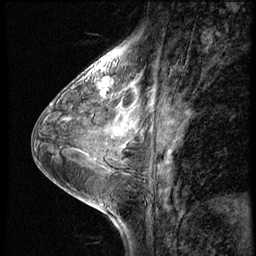
Breast MRI (dynamic contrast-enhanced), one sagittal slice. Position 22 of 56 along the scan axis. 4 images stored at this slice position (order not interpretable as contrast timing). 1.5 T. TE 4.2 ms, TR 8.9 ms. 2.5 mm slice thickness. 256 × 256 image matrix, field of view 200 × 200 mm. Patient: female, 38 years. Case-level facts recorded for this patient, not image findings: setting: breast cancer imaged before/during neoadjuvant chemotherapy; receptor status: triple-negative.
Outlined on this slice (semi-automatic segmentation, software-assisted and operator-edited):
- analysis volume of interest (the breast-tissue region the enhancement analysis was run in; not a lesion): bounding box (x1, y1, x2, y2) in pixels: (88, 73, 115, 102)
- tumour enhancement mask (voxels above the 140 % enhancement threshold inside the analysis volume of interest): (101, 81, 109, 97)